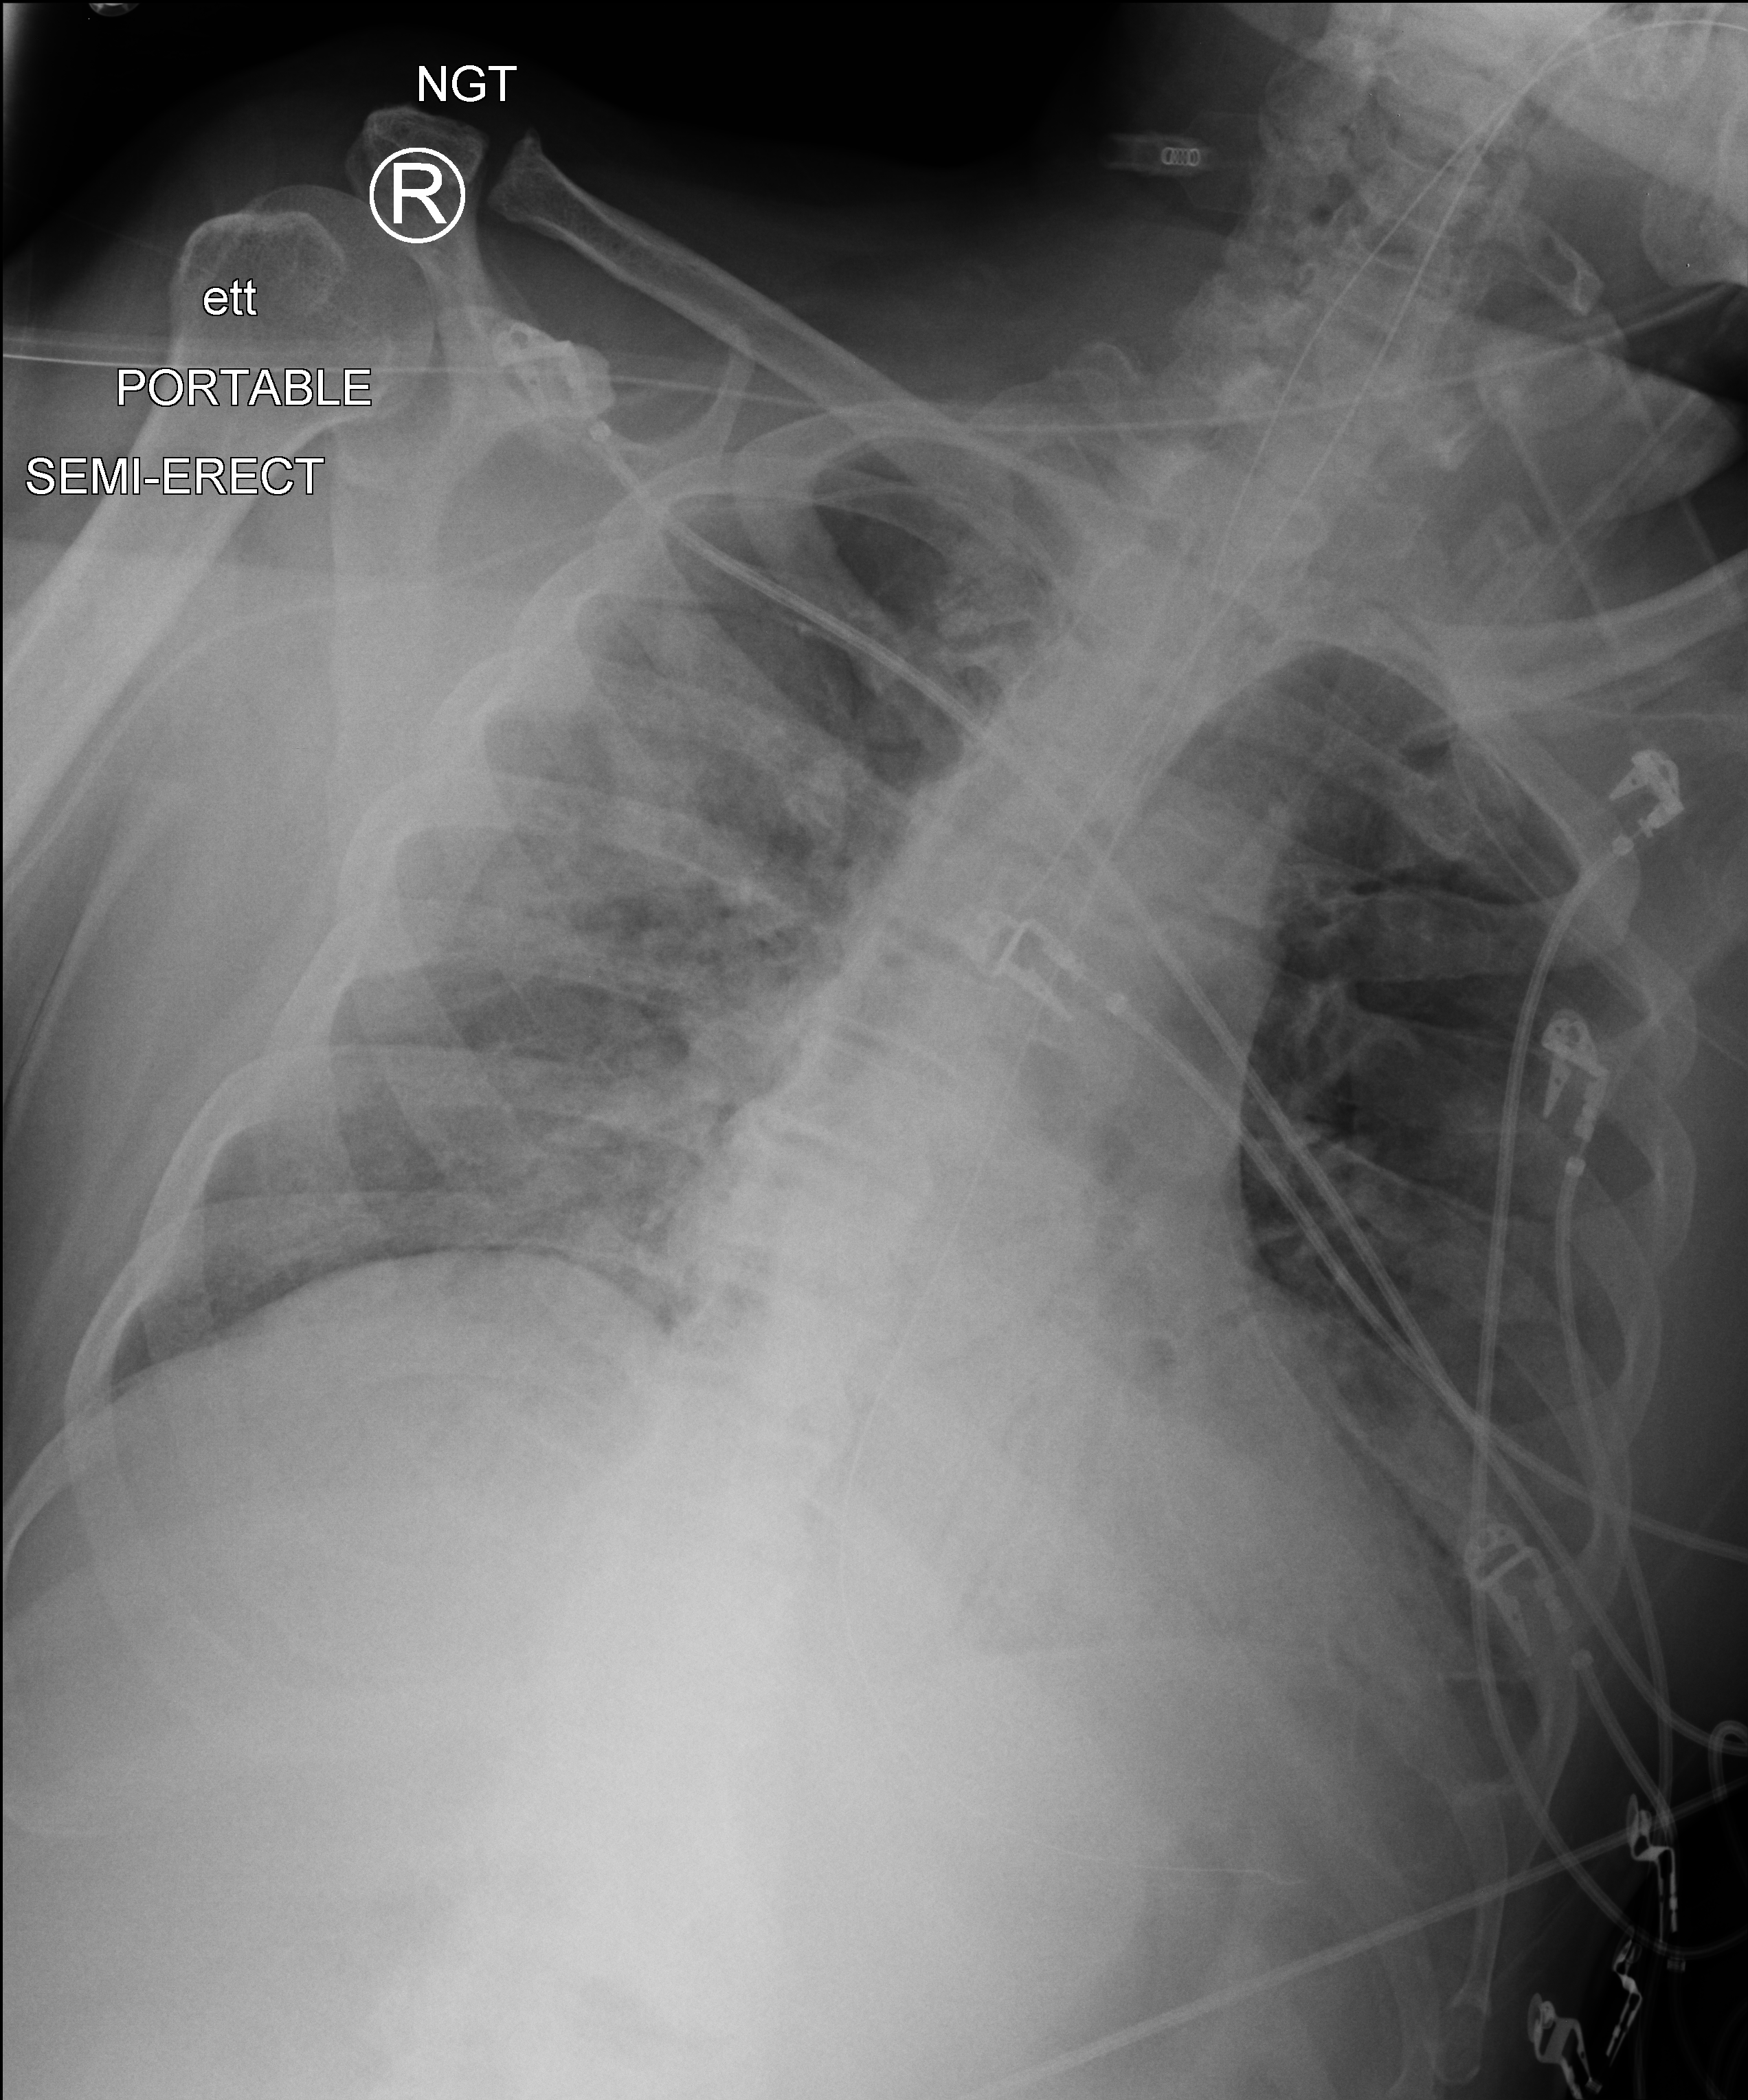
Chest X-ray (portable); anteroposterior (AP) projection. Male patient hospitalised with COVID-19, age 75–90 years.
Admission-level facts for this patient (not findings on this image; timing relative to this image not recorded): length of hospital stay: 33 days.